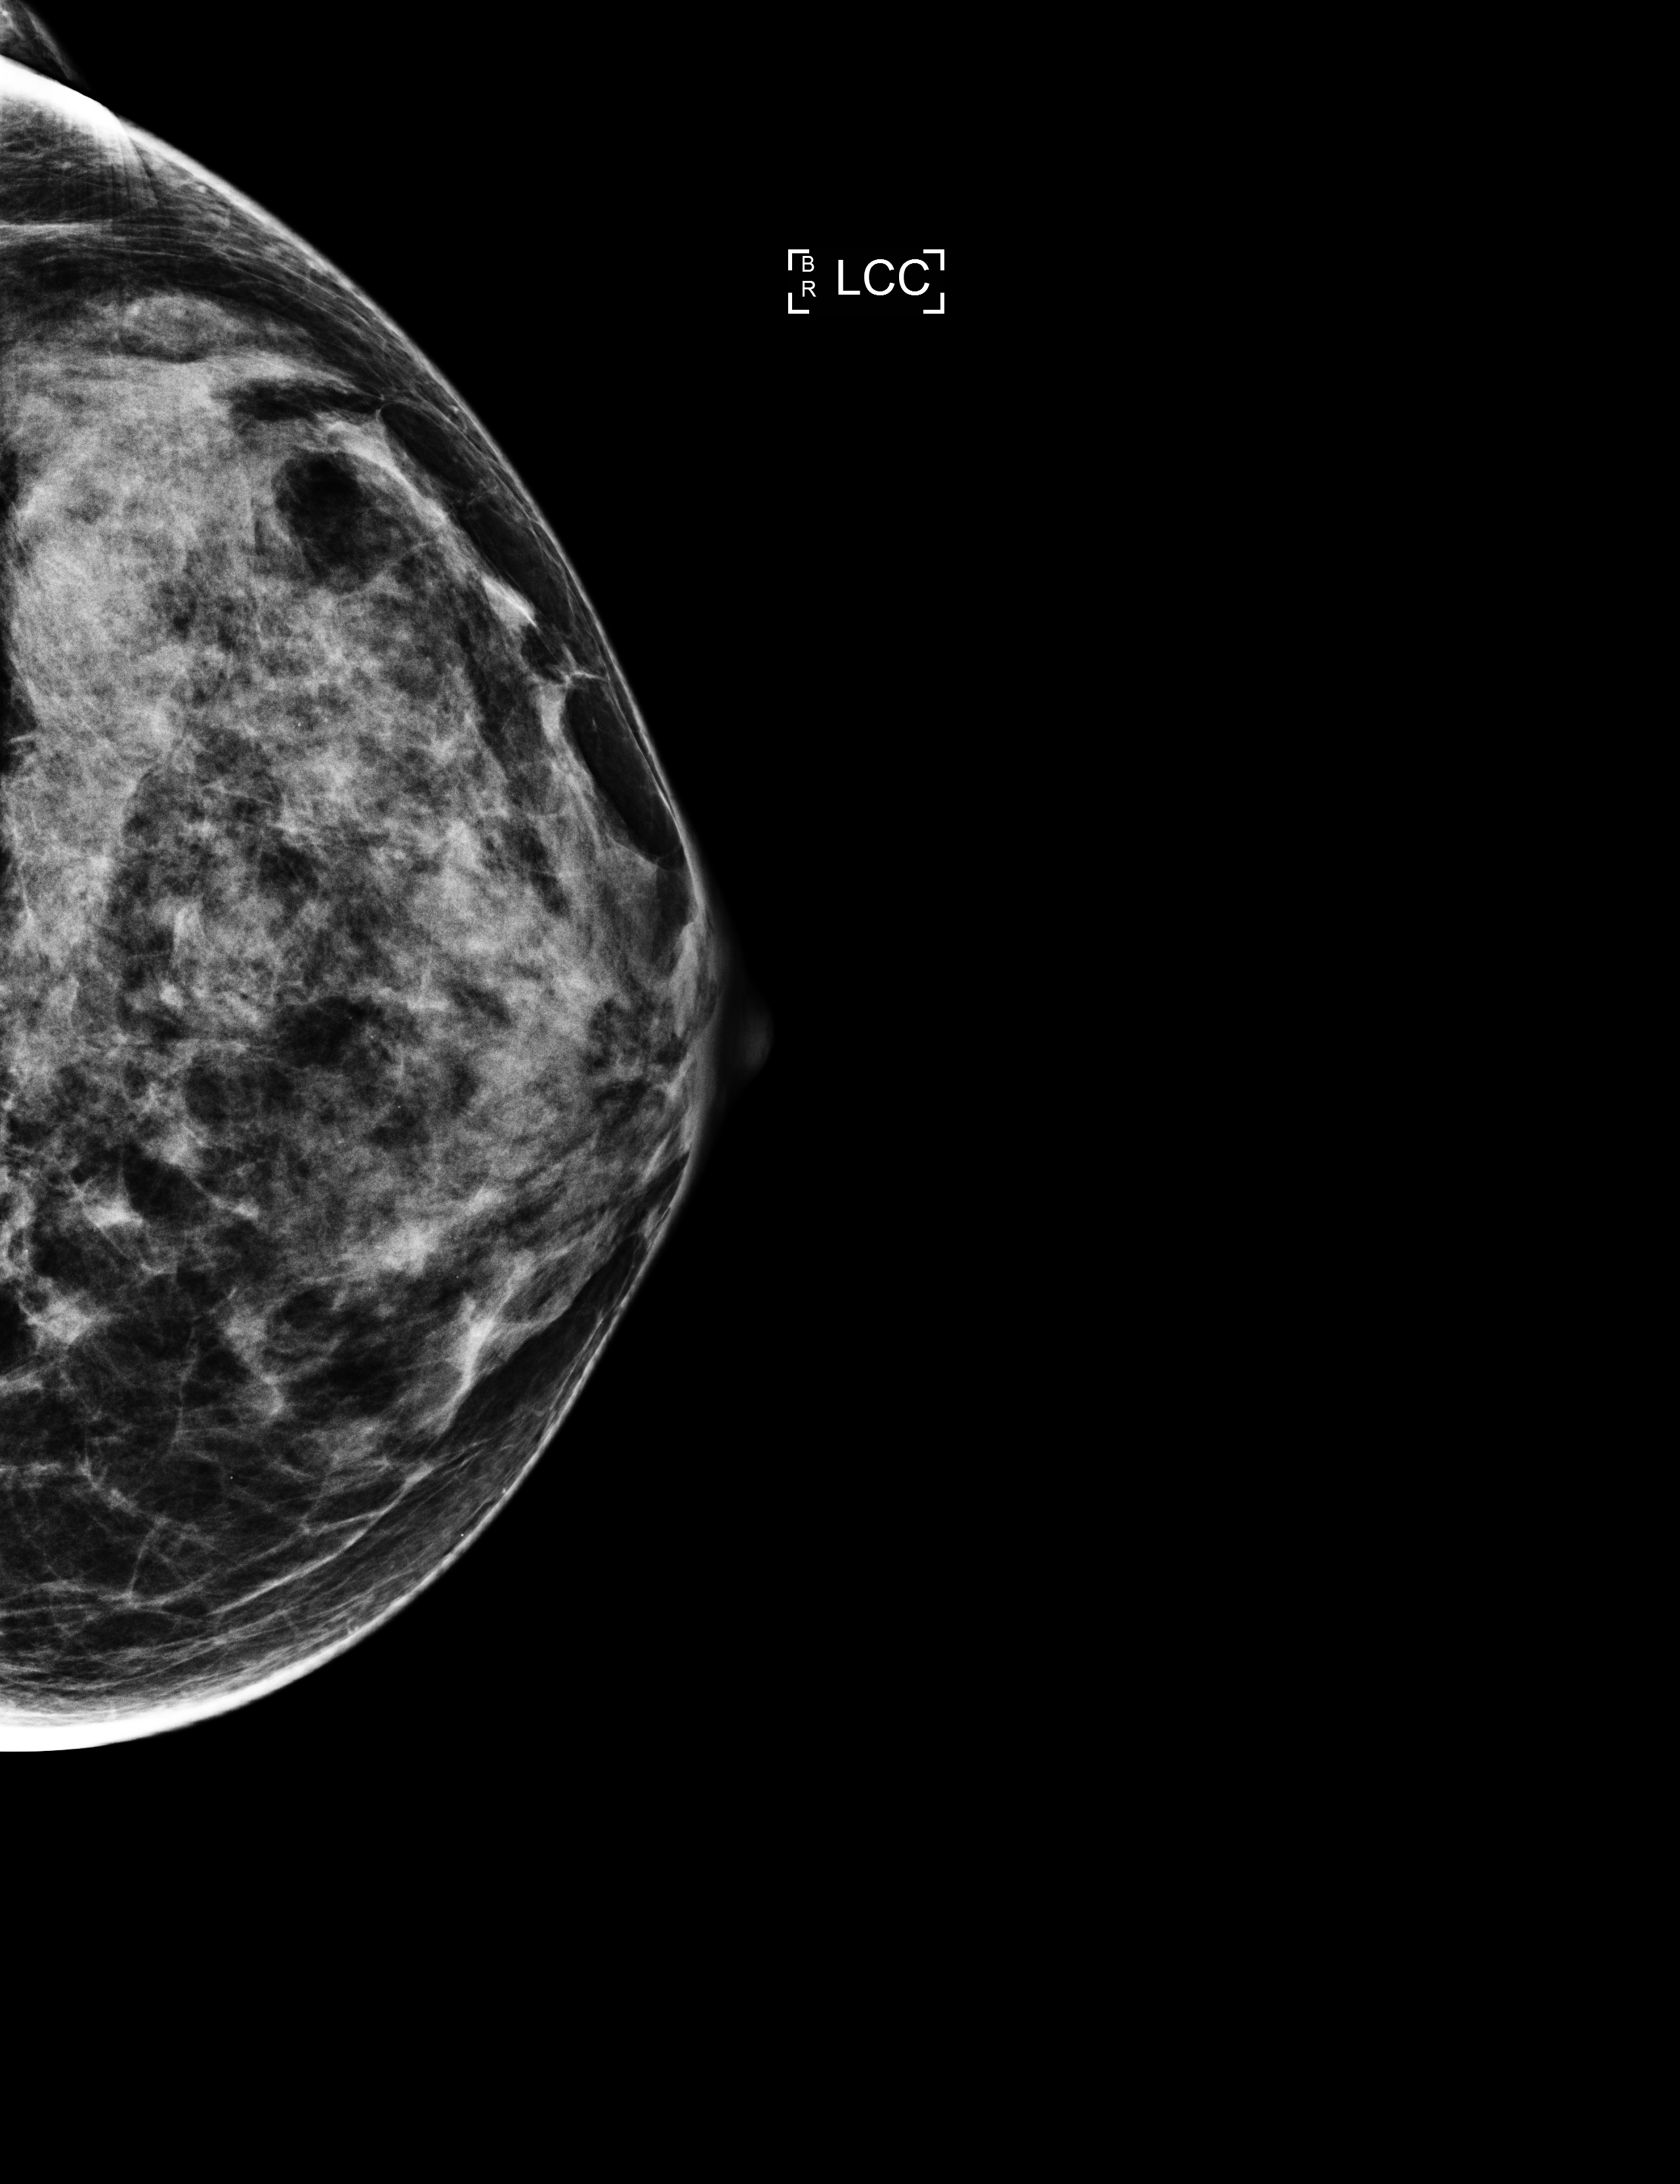
Screening examination. Patient: female, 47 years.
Image type: full-field digital mammogram. Breast: left. Projection: CC view.